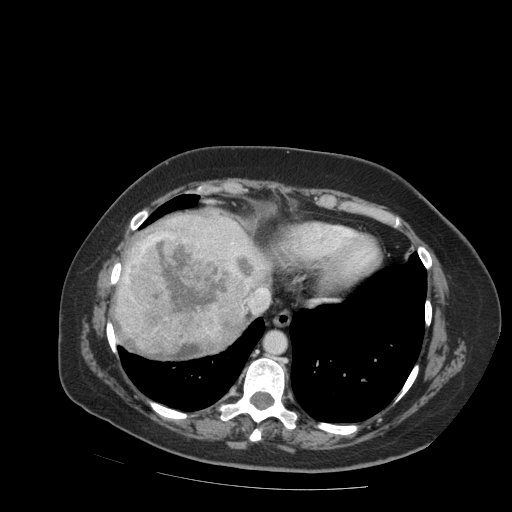
Contrast-enhanced abdominal CT (liver protocol), one axial slice; position 77 of 99 along the scan axis; soft-tissue window (W 400 / L 40 HU); 2.5 mm slice thickness; 512 × 512 image matrix, field of view 400 × 400 mm. From the clinical record (not read from this slice): diagnosis: hepatocellular carcinoma (patient treated with transarterial chemoembolisation; whether this scan precedes or follows treatment is not stated here); TNM stage (as recorded): Stage-IVB; Child-Pugh class: A; tumour differentiation: moderately differentiated; tumour nodularity: uninodular.
Outlined on this slice (semi-automatically segmented with operator editing):
- liver parenchyma outside the tumour (the mass and vessels are separate outlines, so this box may not span the whole liver): box from (x=116, y=212) to (x=270, y=338) px
- mass: (x=113, y=233)–(x=258, y=360)
- liver vessels: (x=173, y=219)–(x=269, y=304)